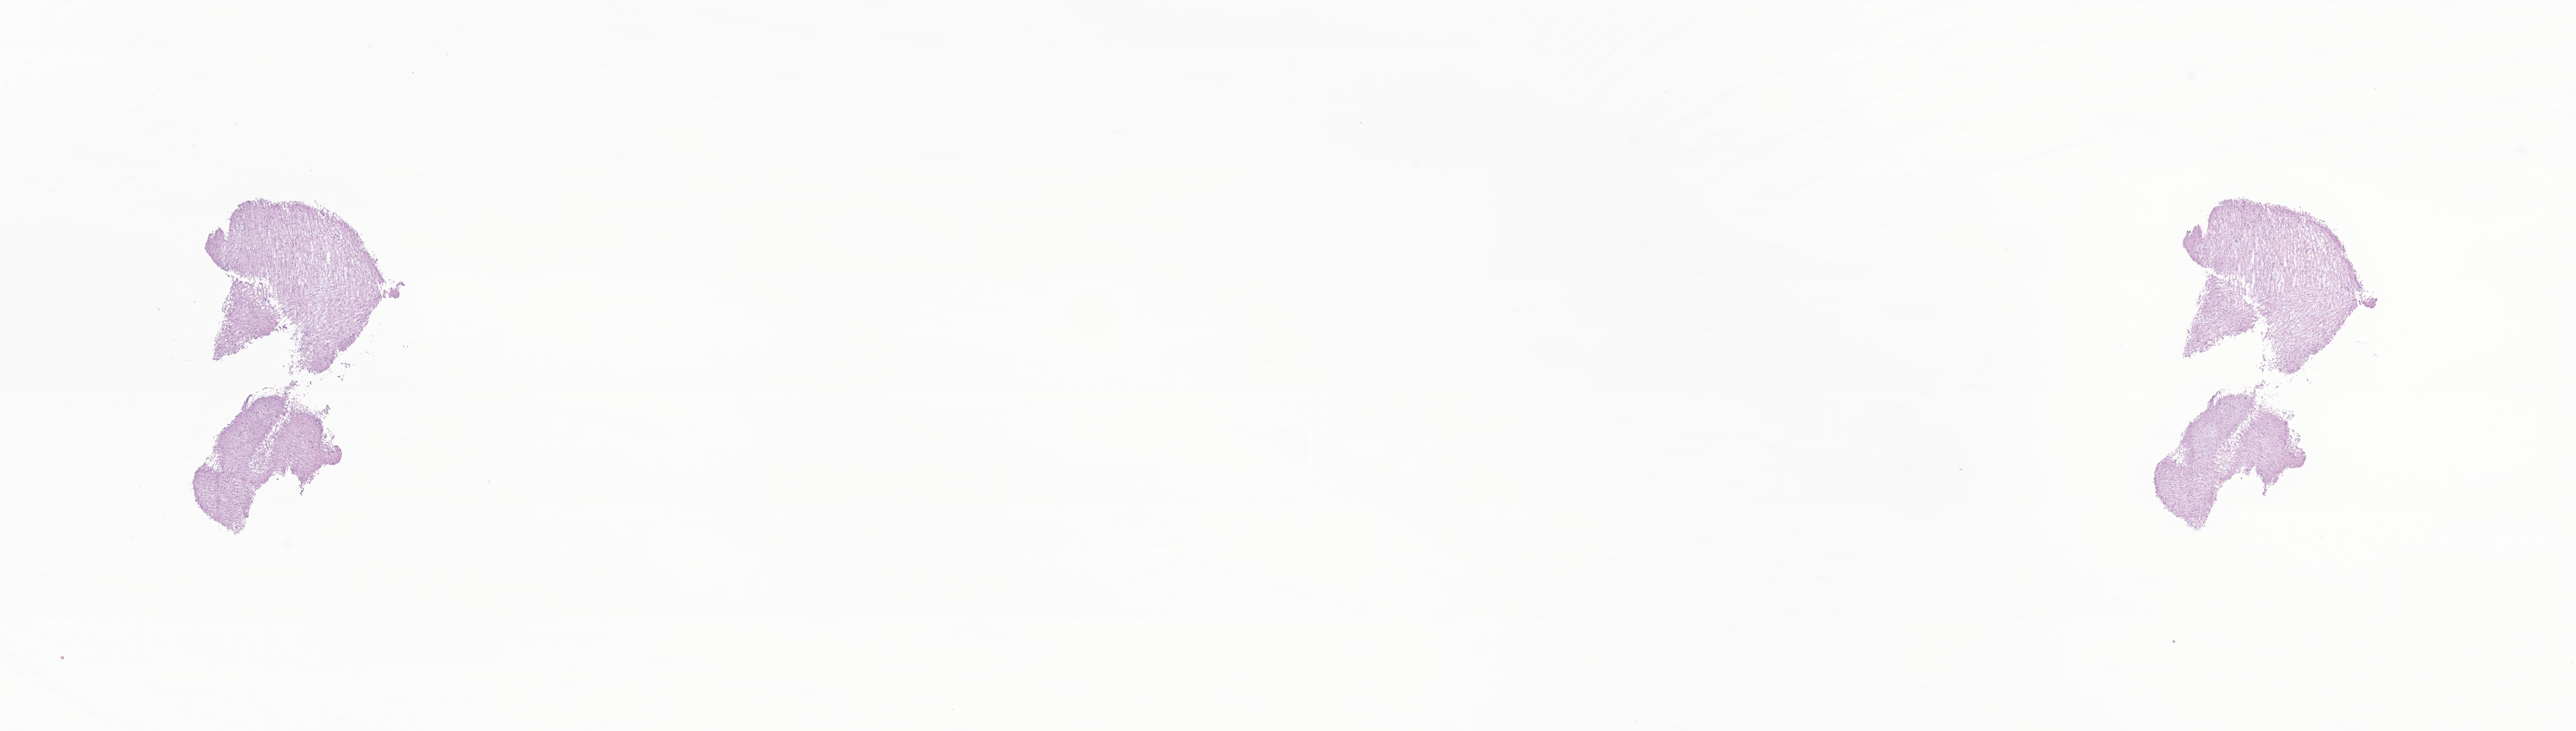
Whole-slide image, haematoxylin and eosin stain of tumor tissue from the brain — shown as a low-resolution overview of the whole scanned area (about 24.2 x 6.9 mm); cryosection (OCT / tissue freezing medium). Patient: male, age 170 months (14 years 2 months).
Recorded diagnosis: Glioma, malignant.